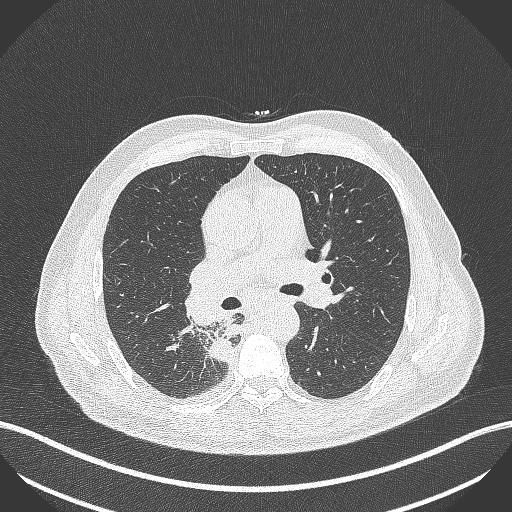
Chest CT, one axial slice; slice 272 of 451 in the series (ordered by position); reconstruction kernel B70f; lung window (W 1500 / L -600 HU); 512 × 512 image matrix. Male patient, age 61 years. Case-level facts recorded for this patient, not image findings: clinical TNM (as recorded): T1 N0 M0; histopathological grade: G3.
Annotated regions visible in this slice (rectangle marked by the reading radiologist):
- lung tumour (recorded histology: small cell carcinoma): box from (x=207, y=336) to (x=240, y=370) px